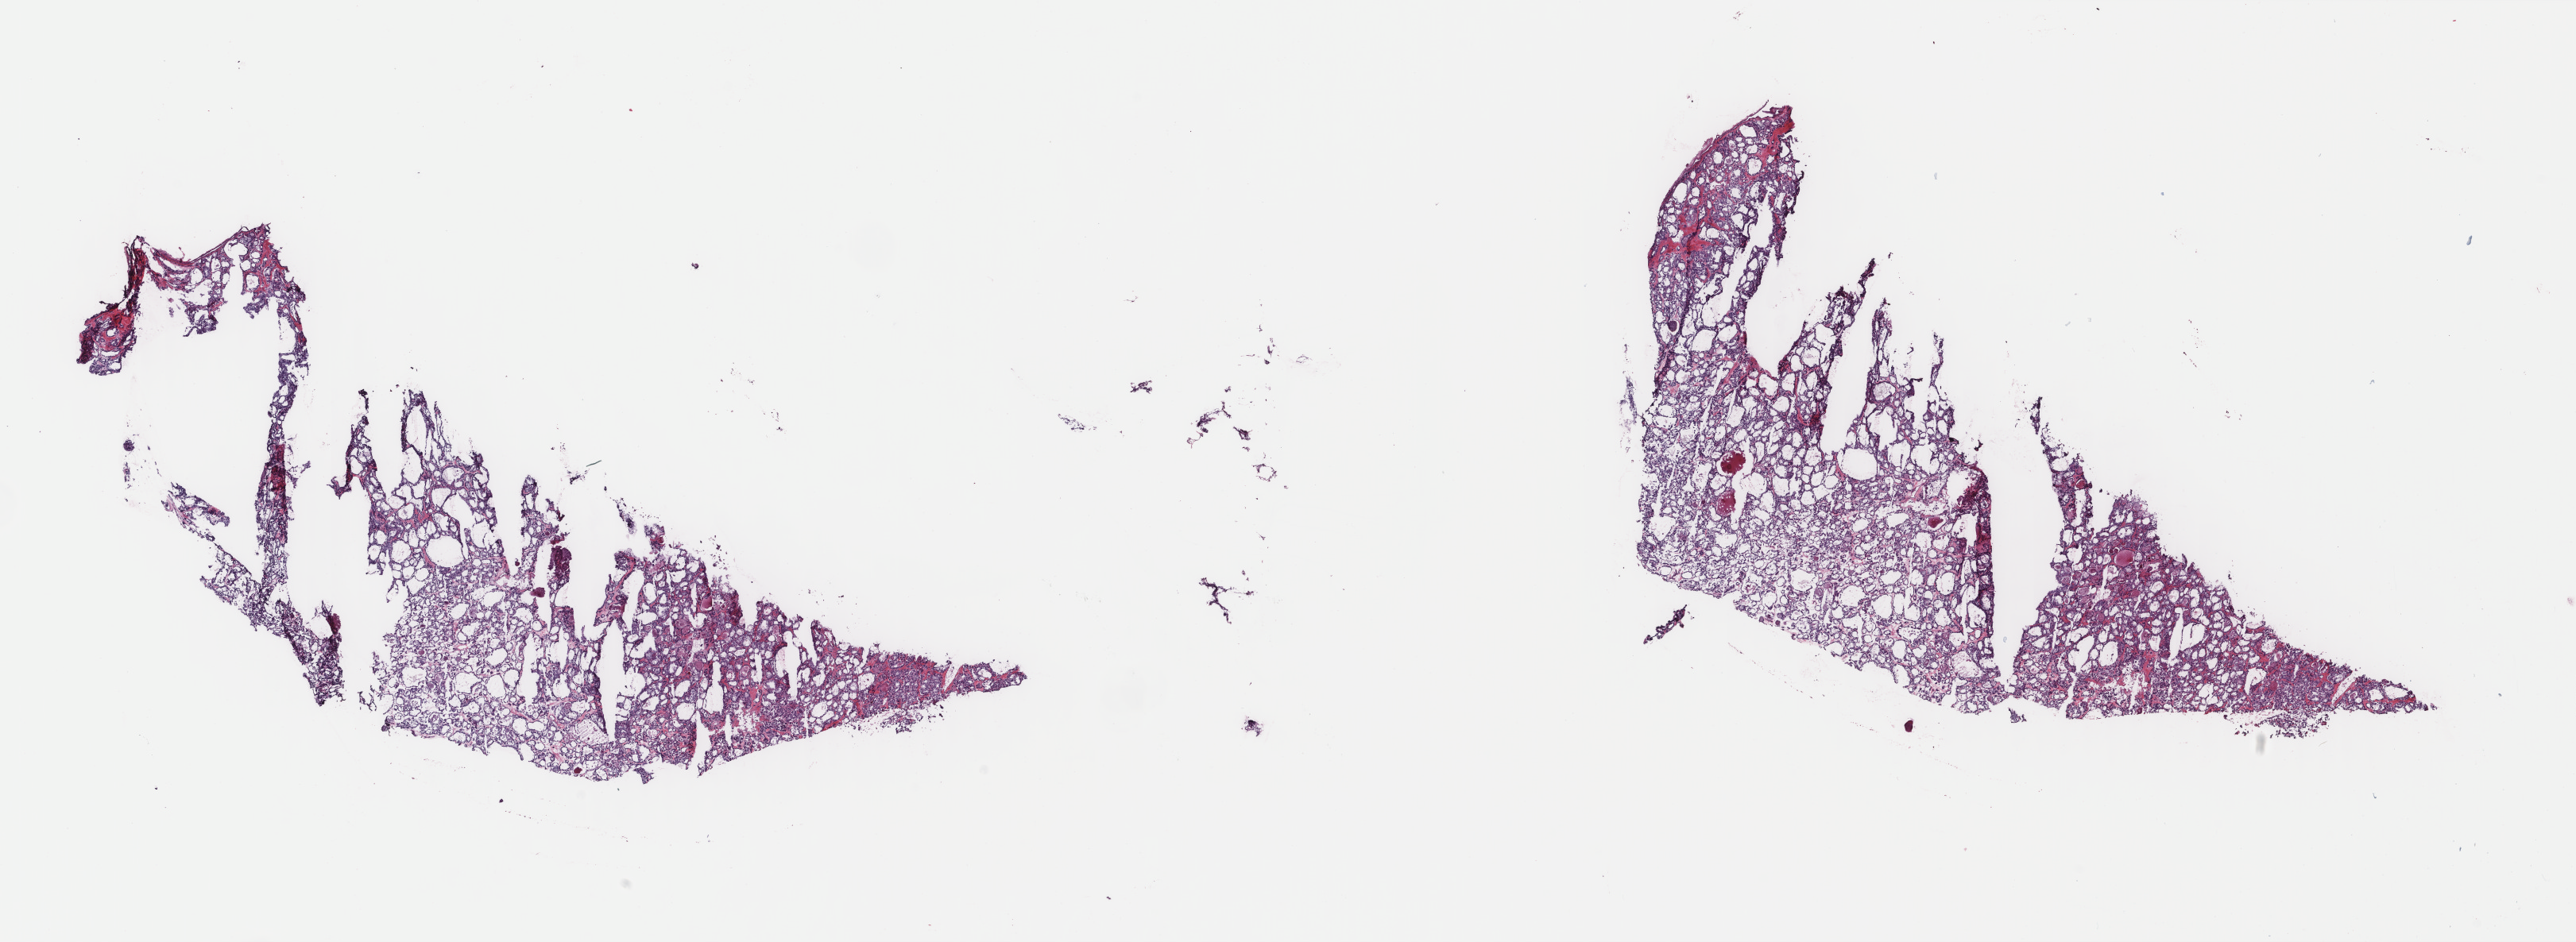
H&E-stained whole-slide image, whole scanned area (about 25.7 x 9.4 mm) shown as a low-resolution overview; frozen section; primary tumour sample from the thyroid. Female patient; age at initial diagnosis 83 years. Slide review estimates, as recorded: tumour cells 100%, tumour nuclei 90%, normal cells 0%, stromal cells 0%, necrosis 0%. Inflammatory infiltration, as recorded: lymphocyte infiltration 0%, monocyte infiltration 0%, neutrophil infiltration 0%.
* AJCC pathologic stage: I
* diagnosis: Papillary carcinoma, follicular variant (thyroid gland)